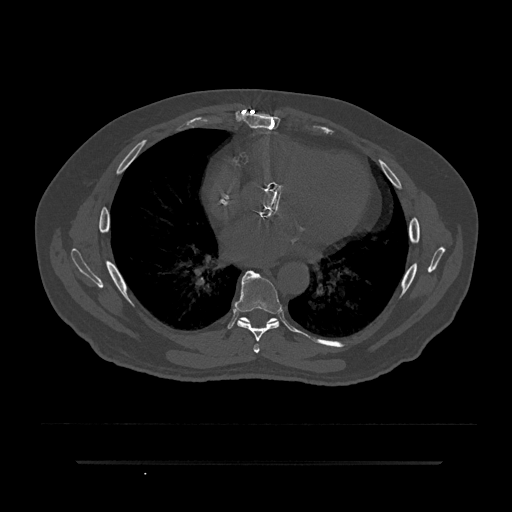
CT including the spine, one axial slice; position 466 of 797 along the scan axis; 120 kVp; bone window (W 1800 / L 400 HU); 0.5 mm slice thickness; 512 × 512 image matrix, field of view 464 × 464 mm. Patient: male, 59 years. From the clinical record (not read from this slice): primary cancer: bile ducts.
Structures marked on this image (semi-automatic segmentation, software-assisted and operator-edited):
- T6 vertebra: box from (x=253, y=344) to (x=260, y=353) px
- T7 vertebra: (x=234, y=270)–(x=281, y=342)
- T8 vertebra: (x=238, y=317)–(x=295, y=332)